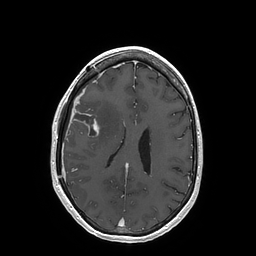
Brain MRI from a brain-tumour surgery series, one axial slice. Slice 67 of 202 in the series (ordered by position). T1-weighted post-contrast. 256 × 256 image matrix, field of view 250 × 250 mm. Case-level facts recorded for this patient, not image findings: histopathology: Glioblastoma; WHO grade: 4; IDH mutation: no.
Outlined on this slice (manually delineated by an expert):
- tumour: box from (x=71, y=108) to (x=99, y=137) px